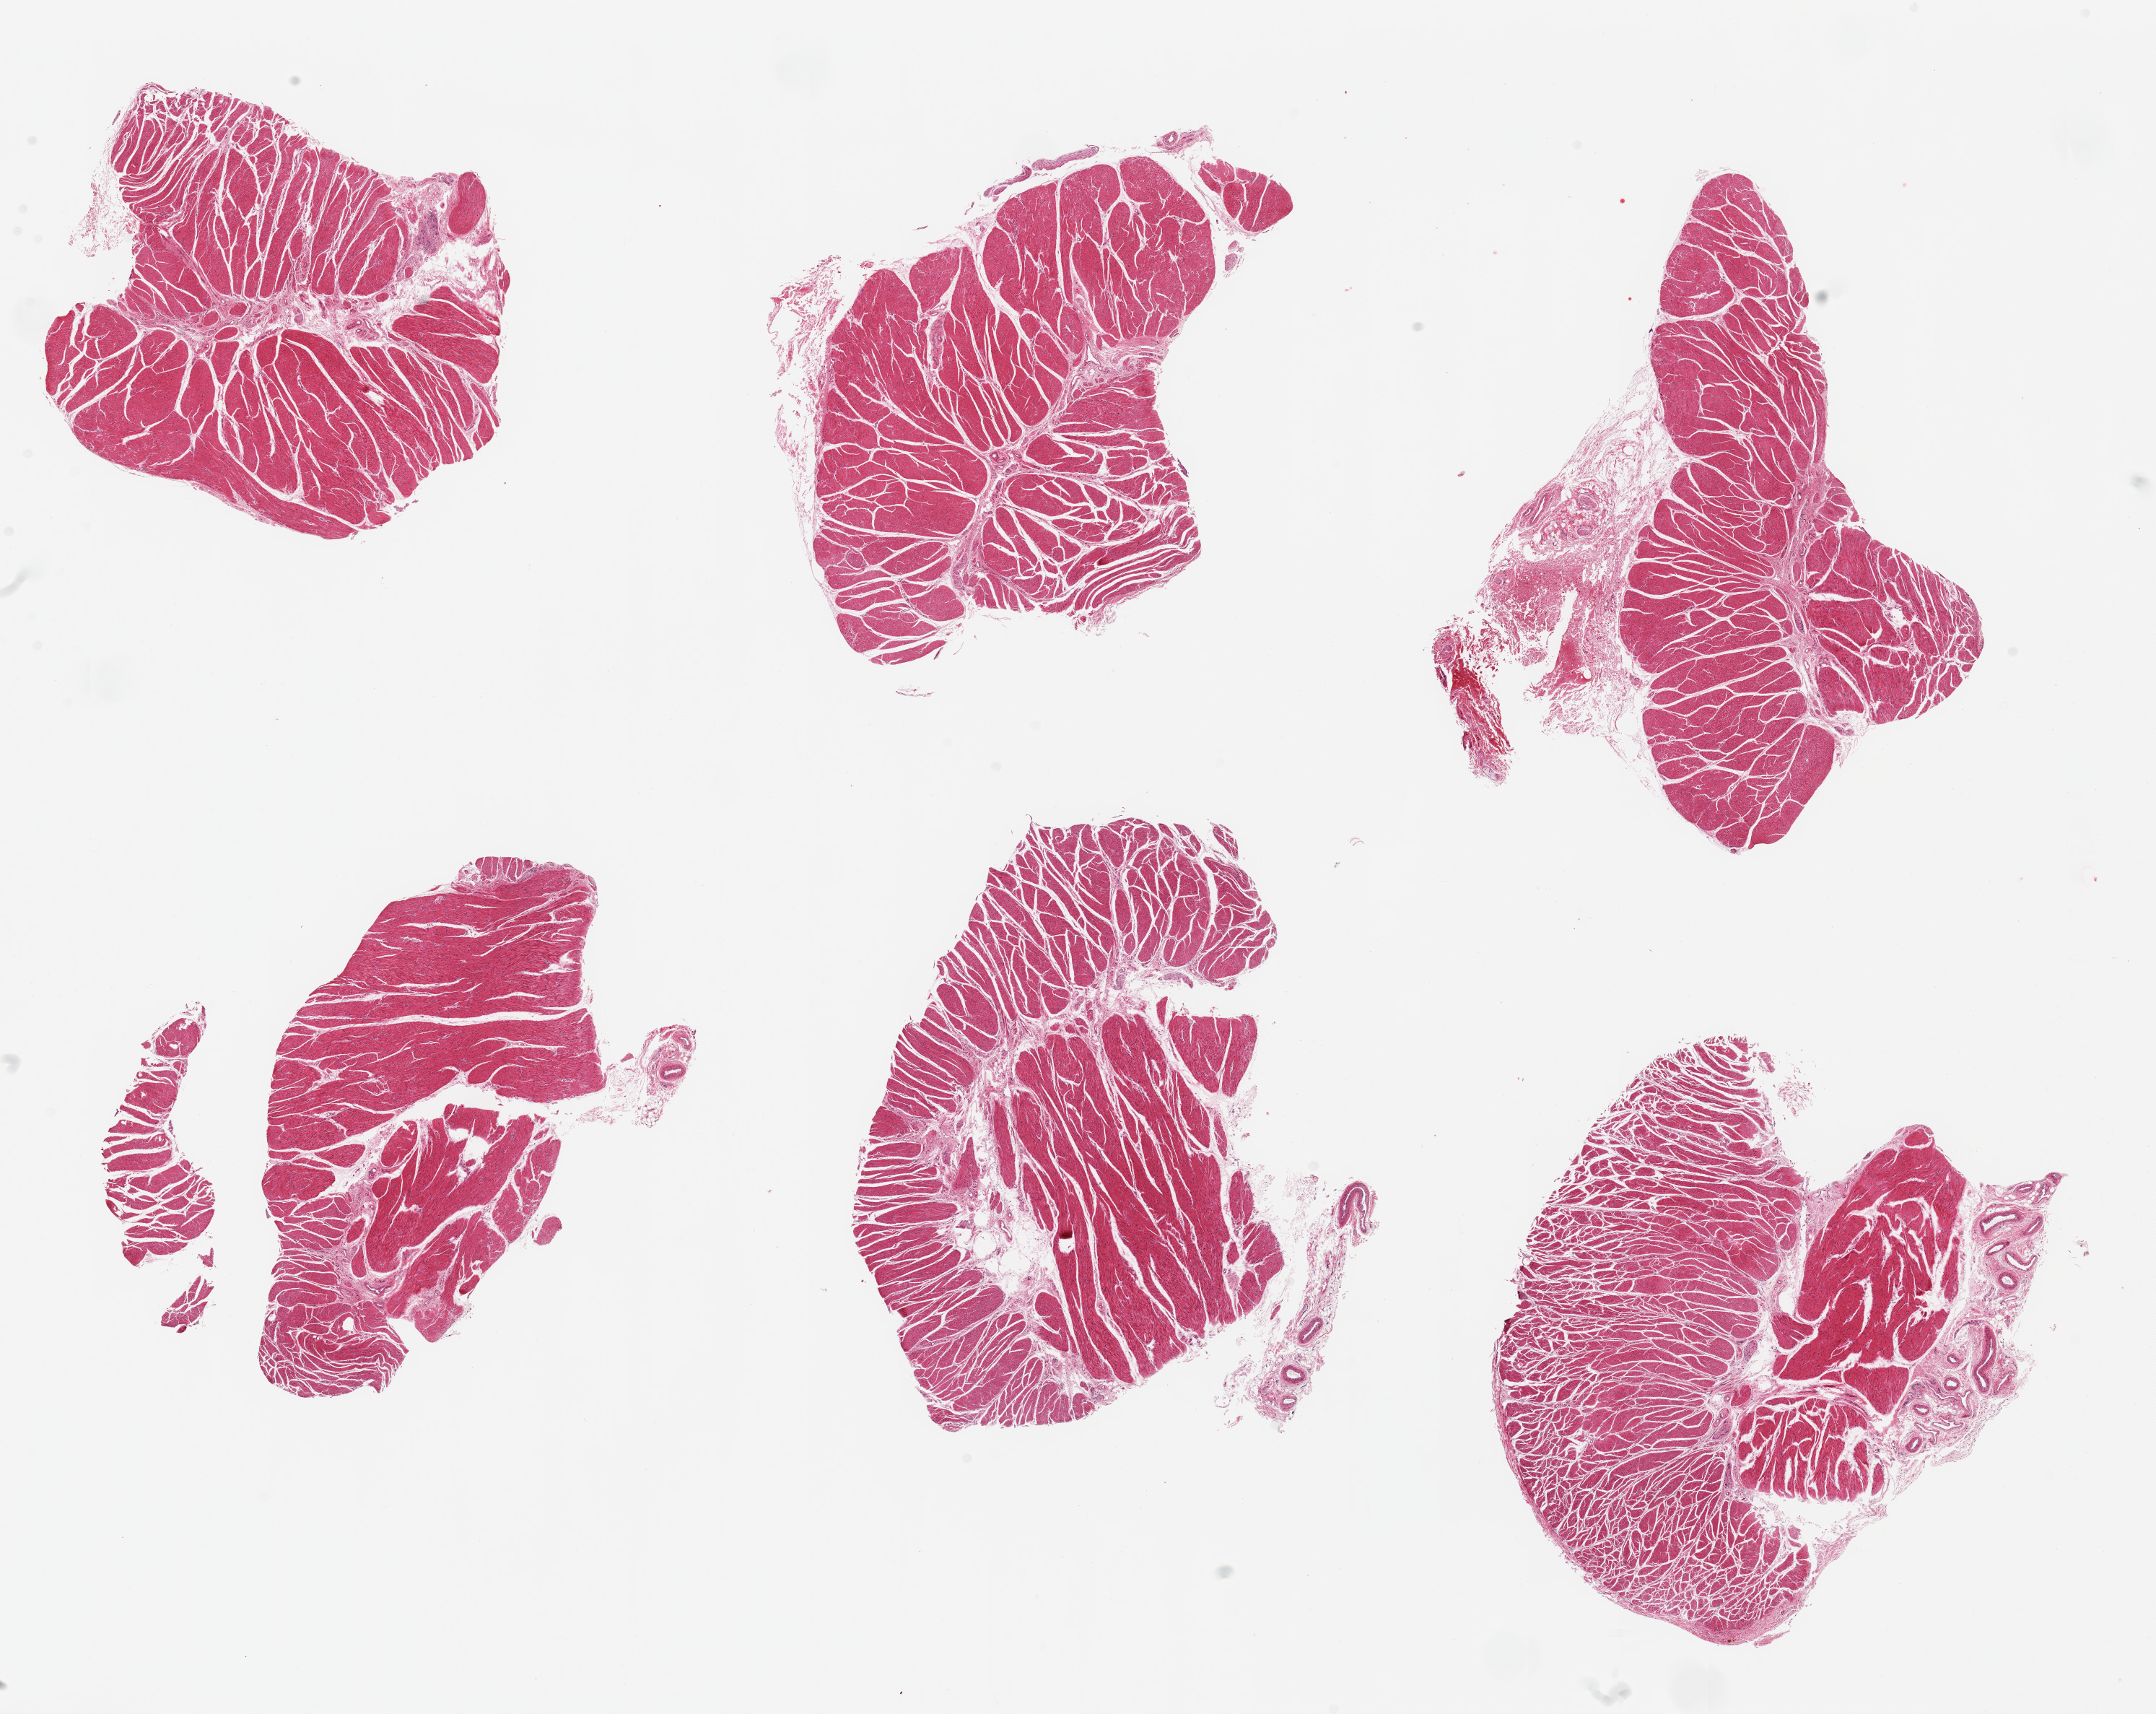
Whole-slide image, hematoxylin and eosin (H&E) stain — shown as a low-resolution overview of the whole scanned area (about 23.6 x 18.8 mm, acquisition: 20x scan), PAXgene-fixed, paraffin-embedded tissue, target tissue: esophageal muscle, tissue donor sample. Donor sex: male.
Pathologist's review note for this sample: 6 pieces, one with adherent fat/serosa.